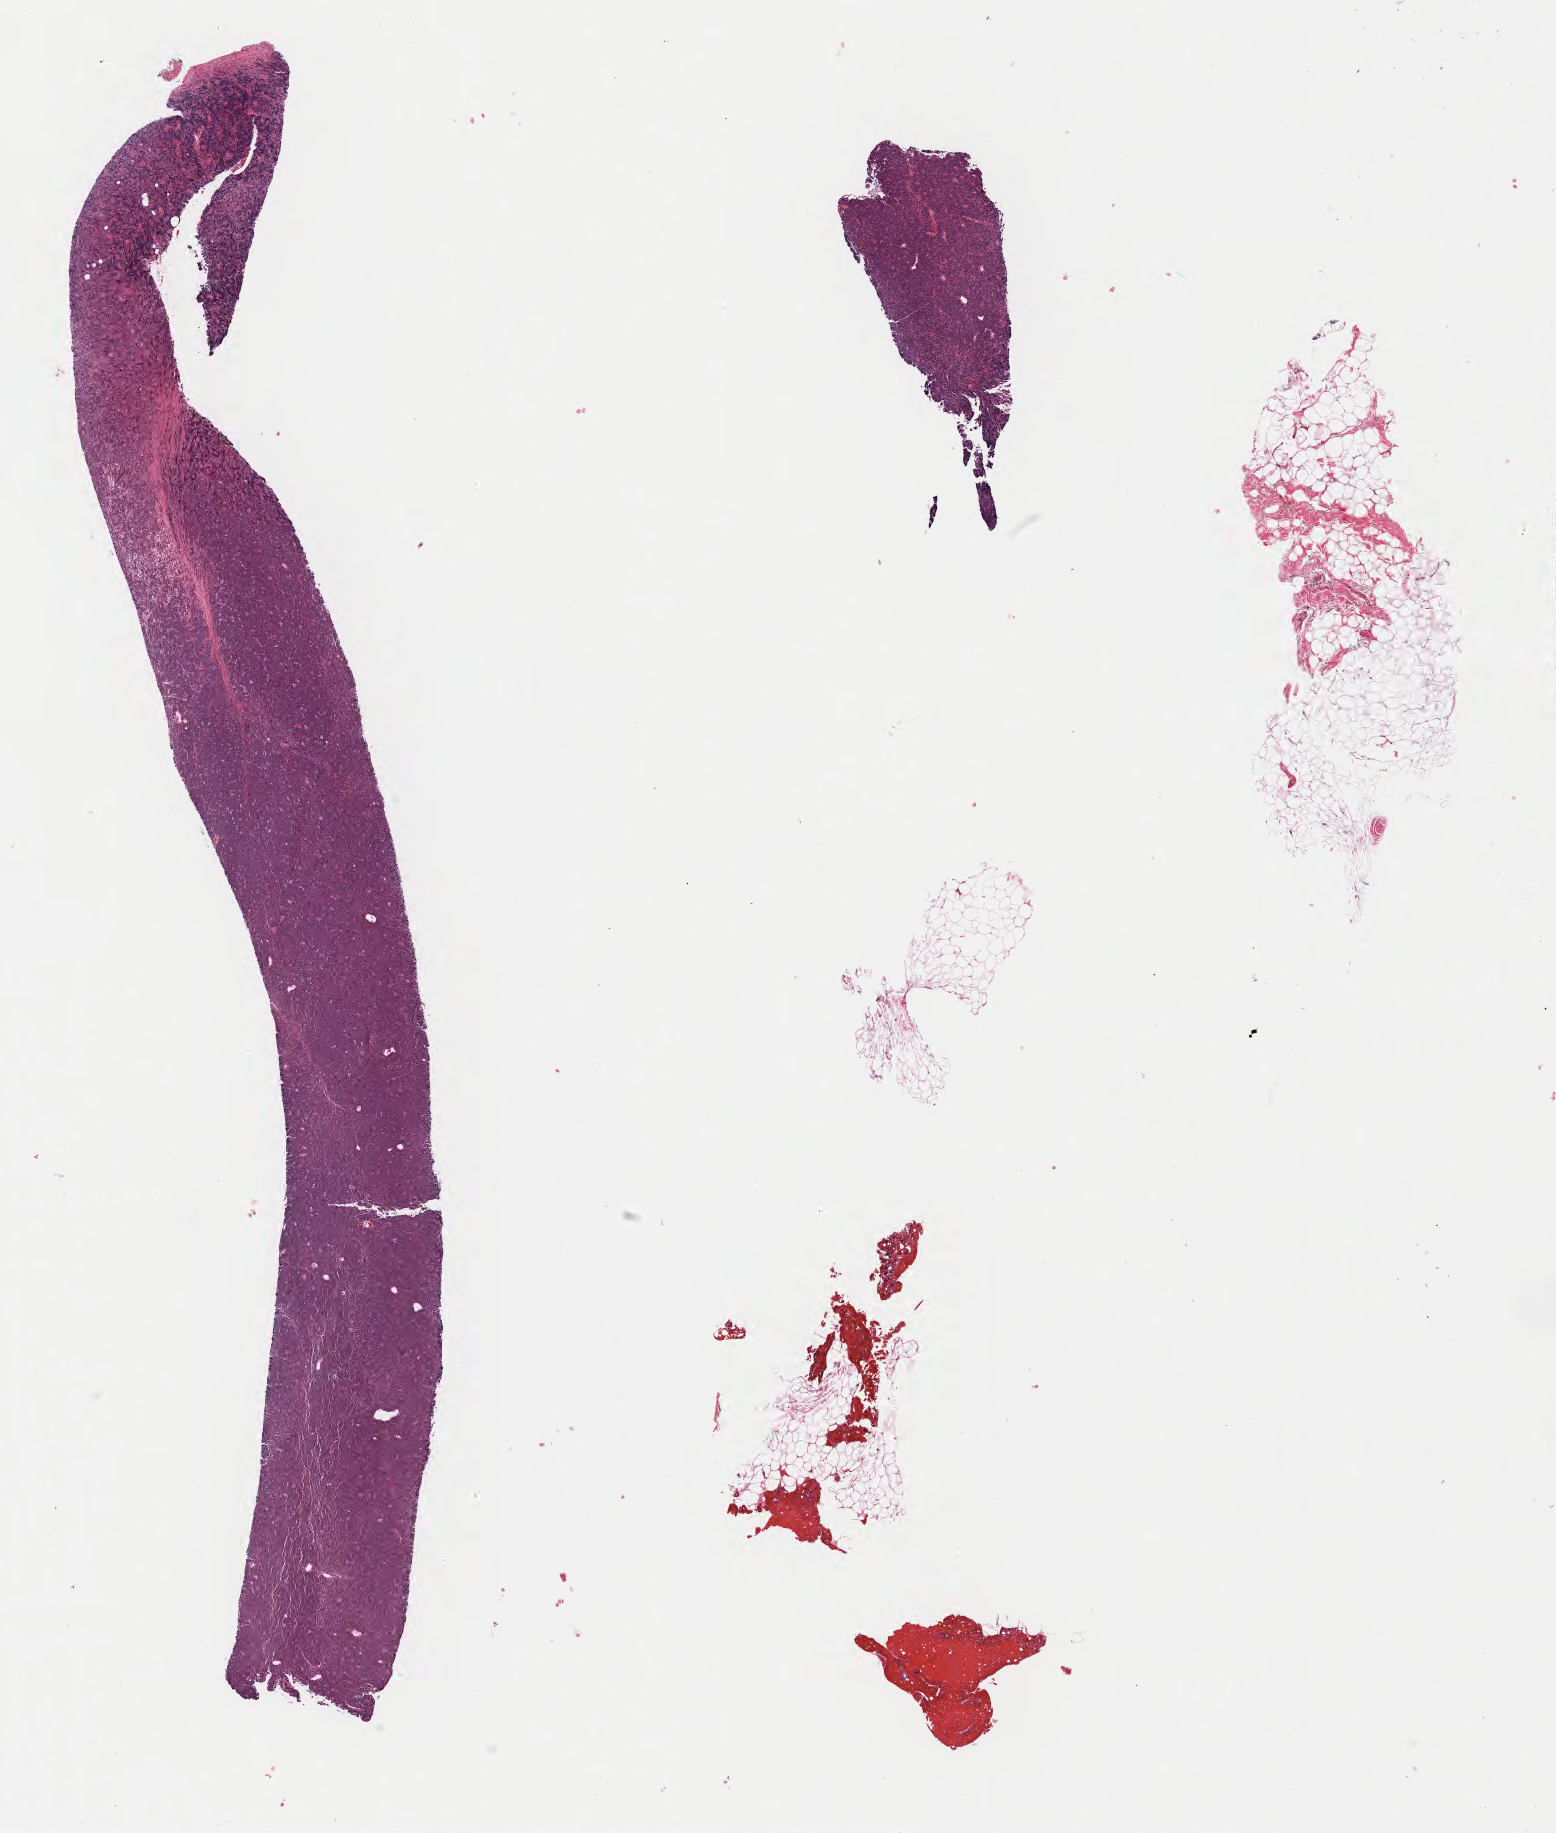
H&E whole-slide image — a low-resolution overview of the entire scanned area, about 12.6 x 14.8 mm. Specimen: tumor tissue. Female patient, age 61 years.
Histologic diagnosis: Burkitt lymphoma, NOS.